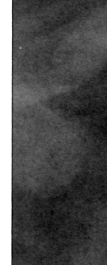
Crop from a digitized film mammogram around one marked abnormality; left breast; CC view; BI-RADS breast density category 1 (scale 1–4).
Marked abnormality: mass, shape lymph node, margins circumscribed; BI-RADS assessment category 2; subtlety rating 4 on a 1 (subtle) to 5 (obvious) scale; benign; no additional work-up was recommended (benign without callback).